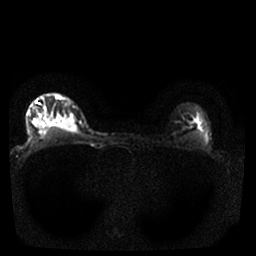
Breast MRI, one axial slice. Position 25 of 25 along the scan axis. Diffusion-weighted series; image 2 of 4 stored at this slice position (different b-values; order by instance number). 1.5 T. 4 mm slice thickness. 256 × 256 image matrix. Female patient.
Structures marked on this image (manually delineated by an expert):
- tumour on diffusion-weighted imaging: bounding box (x1, y1, x2, y2) in pixels: (55, 119, 76, 128)